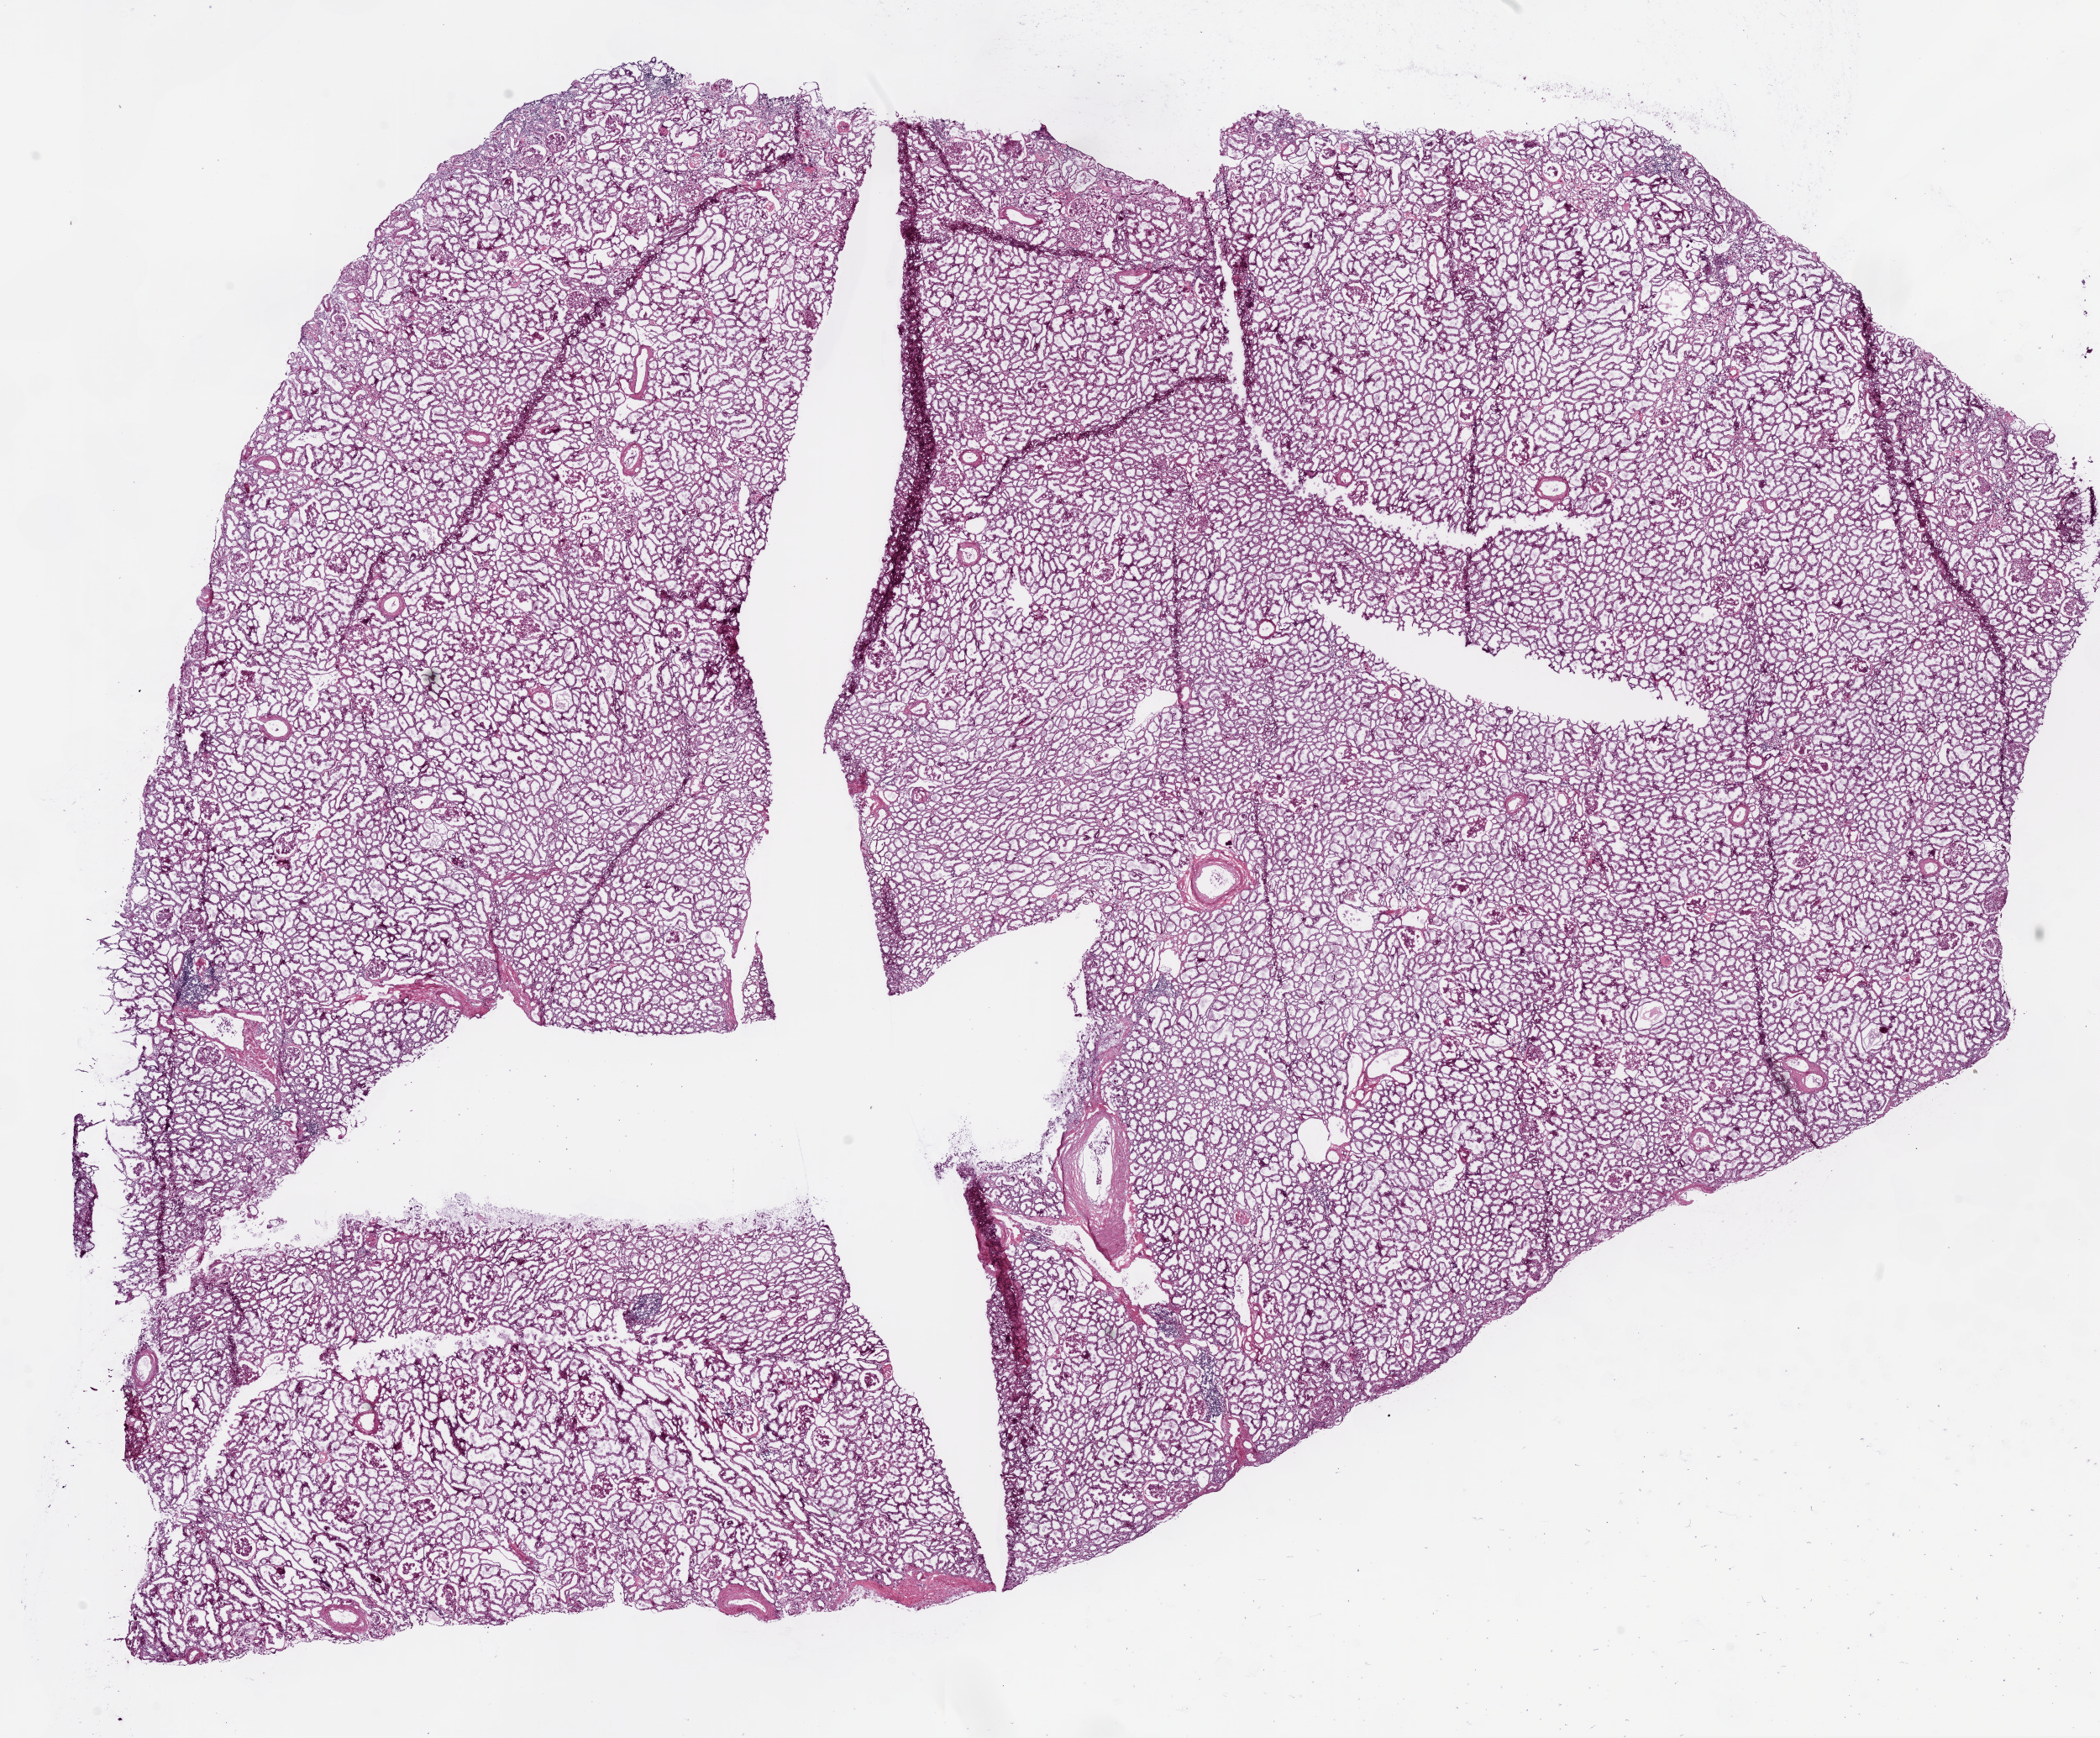
H&E whole-slide image — low-resolution overview of the scanned area, about 20.1 x 16.6 mm (acquisition: 20x scan); frozen section; kidney, solid tissue normal (non-tumour tissue) sample. Patient: male, age at initial diagnosis 67 years.
This section: solid tissue normal sample (biorepository sample class). Patient diagnosis: Clear cell adenocarcinoma, NOS.